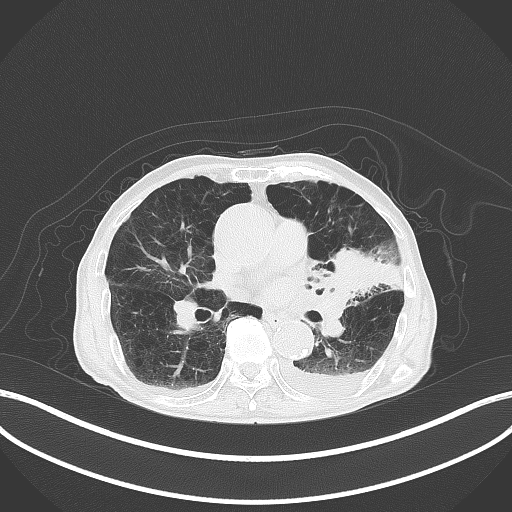
Chest CT, one axial slice; slice 187 of 227 in the series (ordered by position); reconstruction kernel B70f; lung window (W 1500 / L -600 HU); 3 mm slice thickness; 512 × 512 image matrix, field of view 400 × 400 mm. Male patient, age 90 years or older. From the clinical record (not read from this slice): clinical TNM (as recorded): T2b N1 M0.
Annotated regions visible in this slice (bounding box drawn by a radiologist):
- lung tumour (recorded histology: squamous cell carcinoma): bounding box [x1, y1, x2, y2] px = [323, 245, 401, 298]